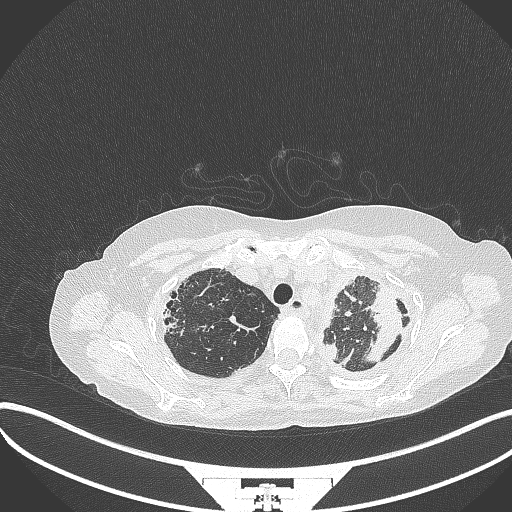
Chest CT, one axial slice; position 282 of 373 along the scan axis; reconstruction kernel B70f; 120 kVp; lung window (W 1500 / L -600 HU); 1 mm slice thickness; 512 × 512 image matrix, field of view 400 × 400 mm. Patient: female, 56 years. Case-level facts recorded for this patient, not image findings: clinical TNM (as recorded): T1 N0 M0.
Annotated regions visible in this slice (rectangle marked by the reading radiologist):
- lung tumour (recorded histology: adenocarcinoma): bounding box (x1, y1, x2, y2) in pixels: (359, 284, 403, 364)